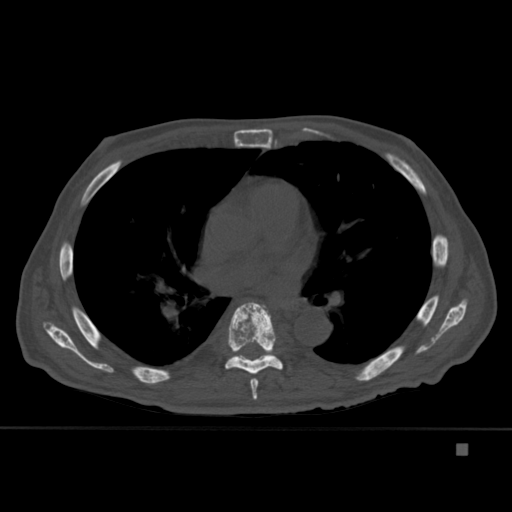
CT including the spine, one axial slice; position 280 of 451 along the scan axis; bone window (W 1800 / L 400 HU); 1.5 mm slice thickness; 512 × 512 image matrix. Patient: male, 75 years. Case-level facts recorded for this patient, not image findings: primary cancer: prostate.
Structures marked on this image (semi-automatically segmented with operator editing):
- T4 vertebra: box from (x=270, y=320) to (x=275, y=334) px
- T6 vertebra: (x=250, y=378)–(x=259, y=400)
- T7 vertebra: (x=225, y=302)–(x=283, y=375)
- T8 vertebra: (x=232, y=354)–(x=272, y=359)